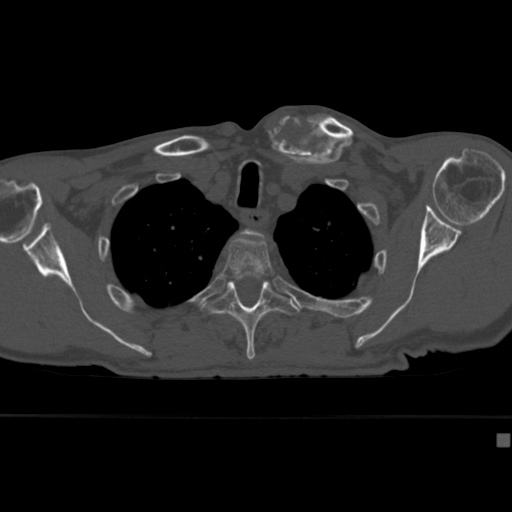
CT including the spine, one axial slice; slice 326 of 430 in the series (ordered by position); 120 kVp; bone window (W 1800 / L 400 HU); 1.5 mm slice thickness; 512 × 512 image matrix, field of view 337 × 337 mm. Patient: male, 64 years. Case-level facts recorded for this patient, not image findings: primary cancer: uterus; vertebrae with lytic lesions (as recorded): T1, T4, T5, T7, L5.
Outlined on this slice (semi-automatically segmented with operator editing):
- T2 vertebra: bounding box (x1, y1, x2, y2) in pixels: (241, 229, 265, 237)
- T3 vertebra: (222, 237, 274, 282)
- T4 vertebra: (202, 281, 300, 360)